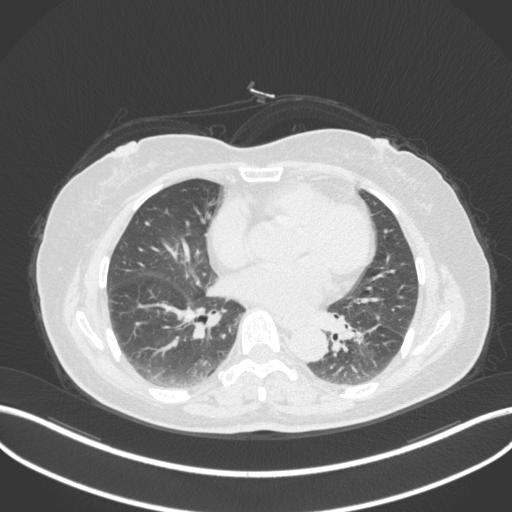
Chest CT, one axial slice. Slice 168 of 307 in the series (ordered by position). Reconstruction kernel B31f. 120 kVp. Lung window (W 1500 / L -600 HU). 1 mm slice thickness. 512 × 512 image matrix, field of view 400 × 400 mm. Female patient, age 59 years. From the clinical record (not read from this slice): clinical TNM (as recorded): T2a N0 M0; histopathological grade: G2-3.
Annotated regions visible in this slice (rectangle marked by the reading radiologist):
- lung tumour (recorded histology: adenocarcinoma): box from (x=350, y=319) to (x=380, y=350) px